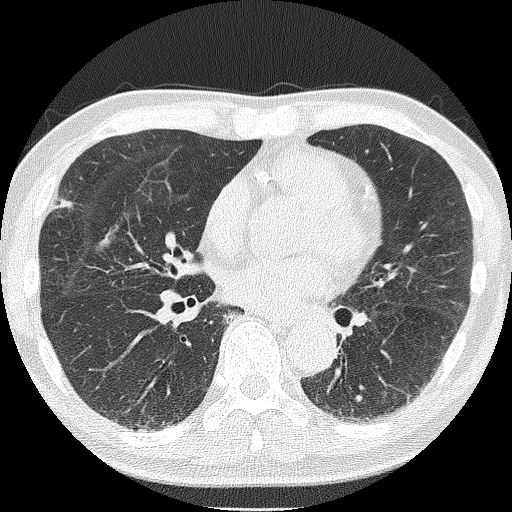
Low-dose screening chest CT, one axial slice; position 89 of 181 along the scan axis; reconstruction kernel FC51; 120 kVp; lung window (W 1500 / L -600 HU); 2 mm slice thickness; 512 × 512 image matrix, field of view 287 × 287 mm.
Structures marked on this image (outlined manually by an expert reader):
- lesion 1 (tumor, upper lobe of right lung): bounding box <56,198,77,212> (left, top, right, bottom; pixels)